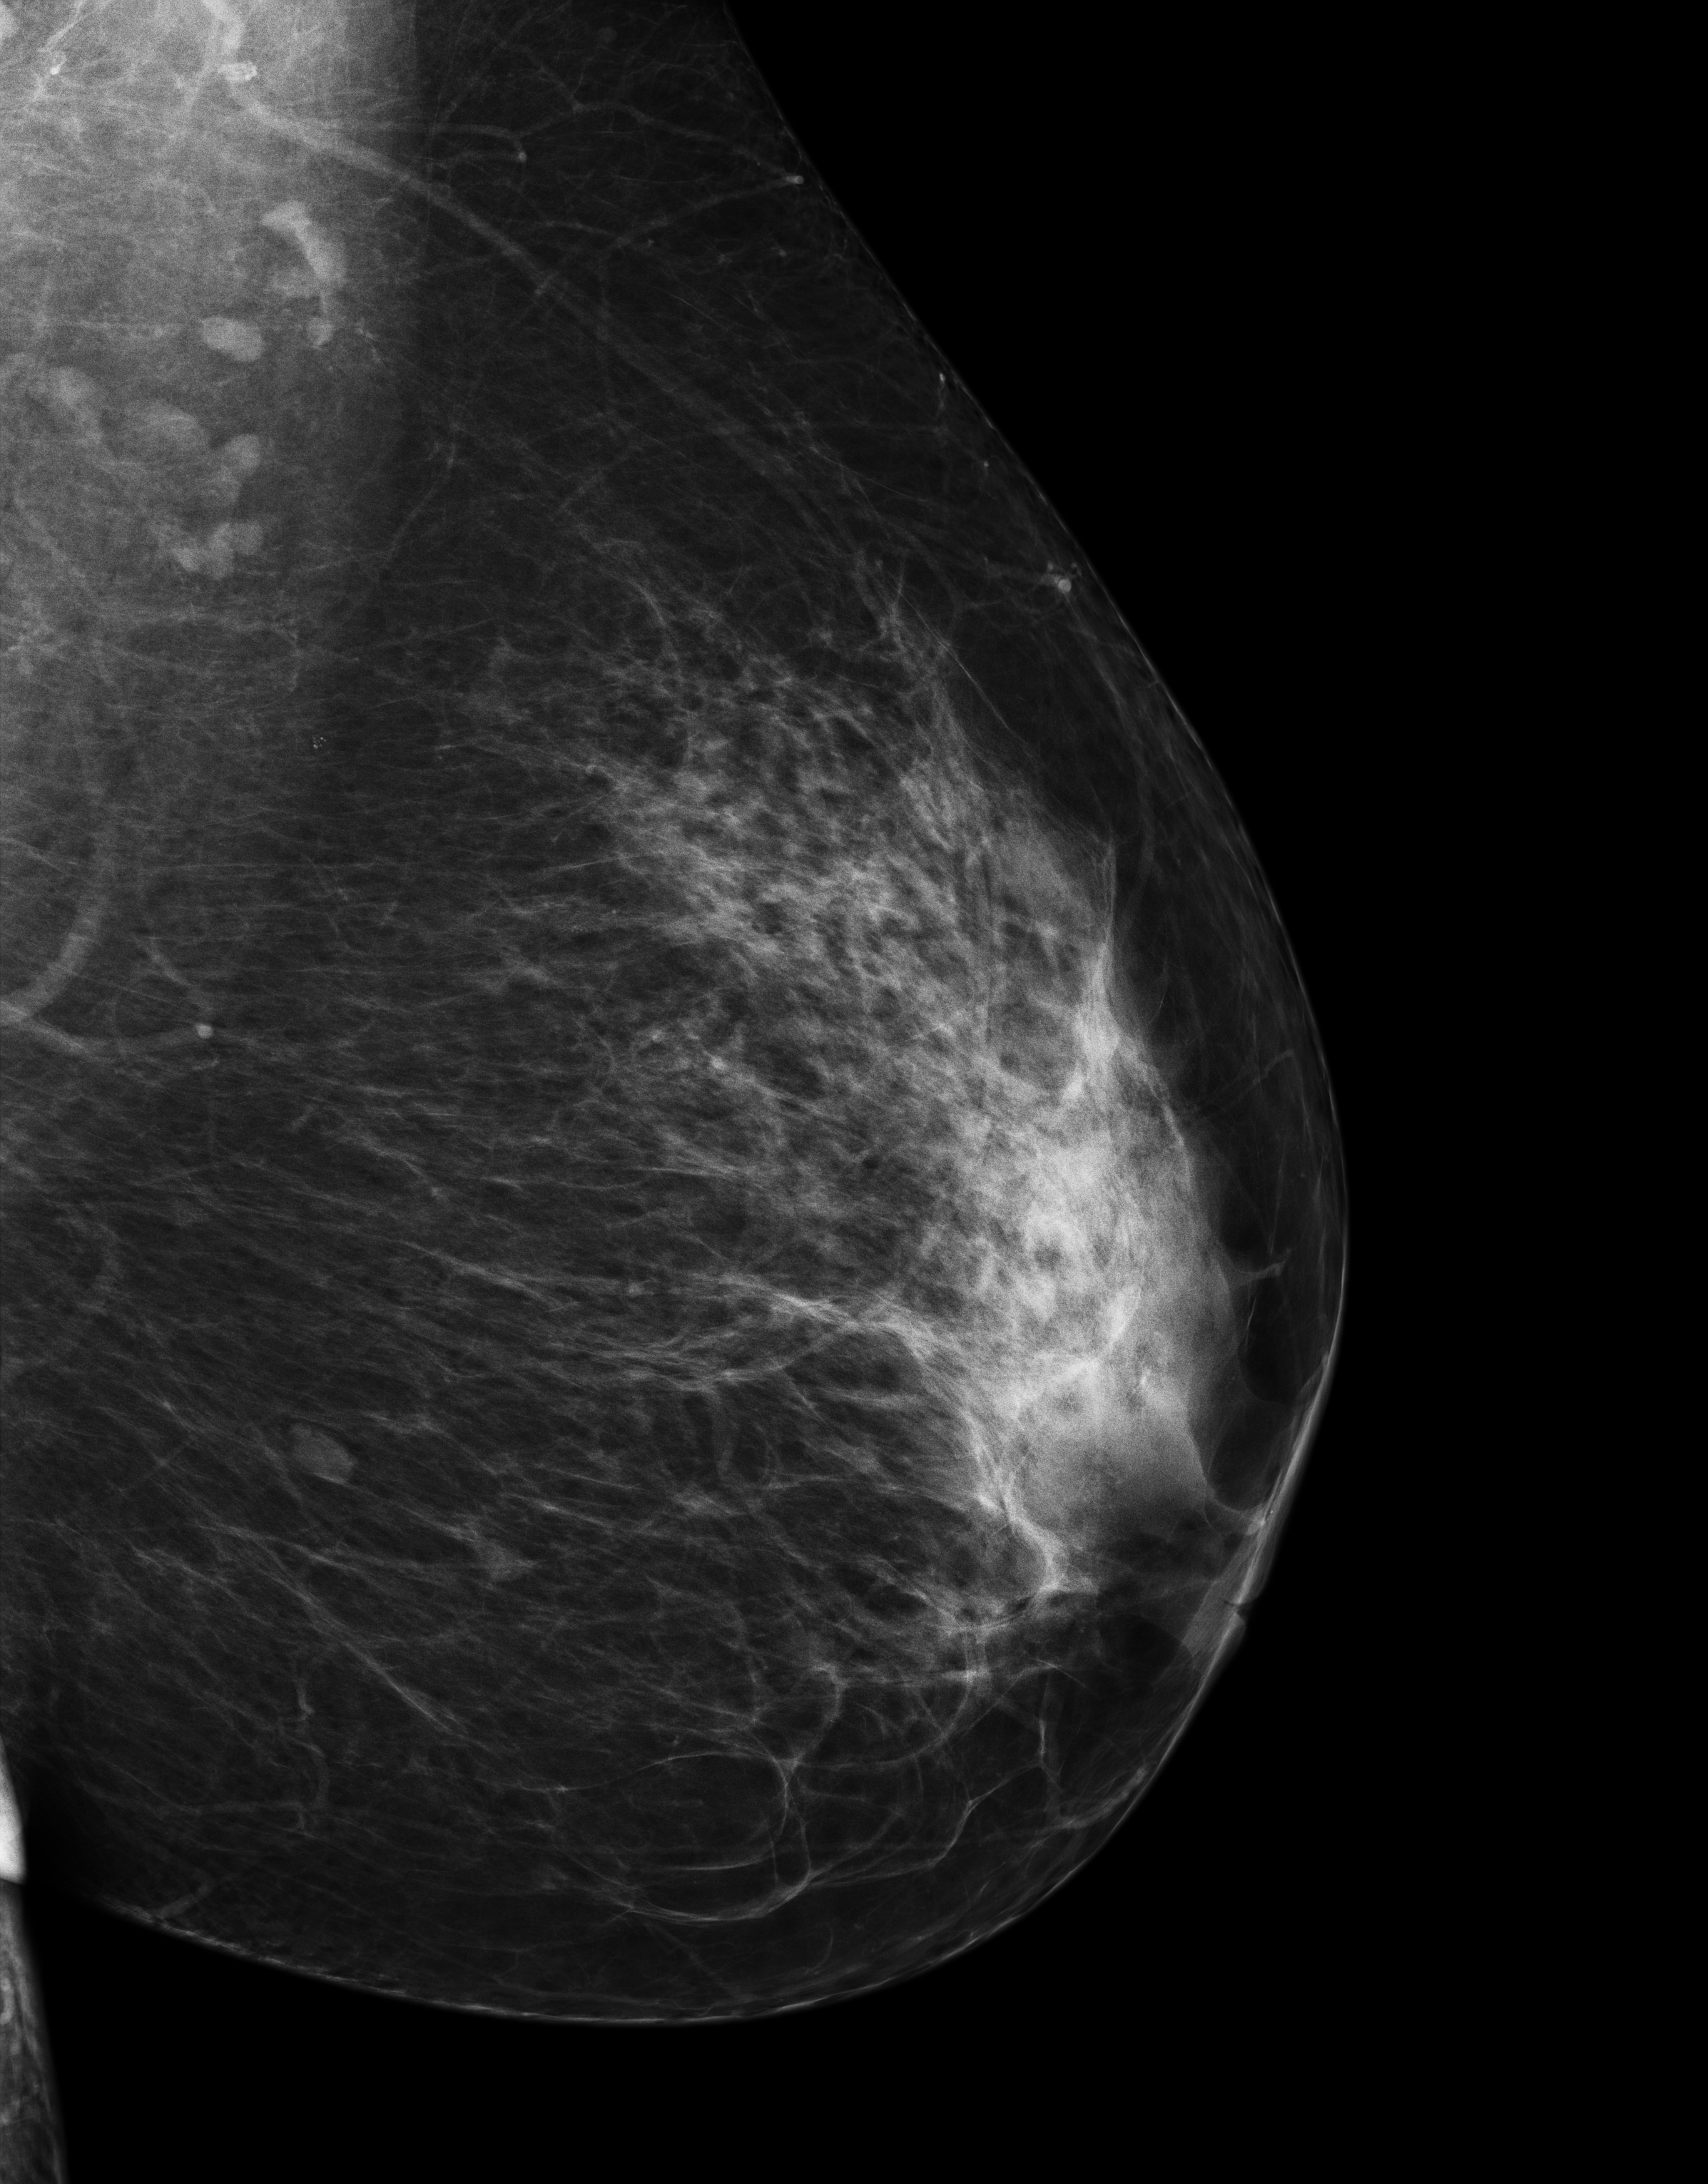
Digital mammogram (FFDM); left breast; MLO view; annual screening mammography examination. Patient: female, 56 years.
- BI-RADS breast density category at the screening exam (both breasts, scale 1–4): 3
- final BI-RADS assessment for this screening round (tomosynthesis exam, both breasts): category 1
- recall: no recall after this screen